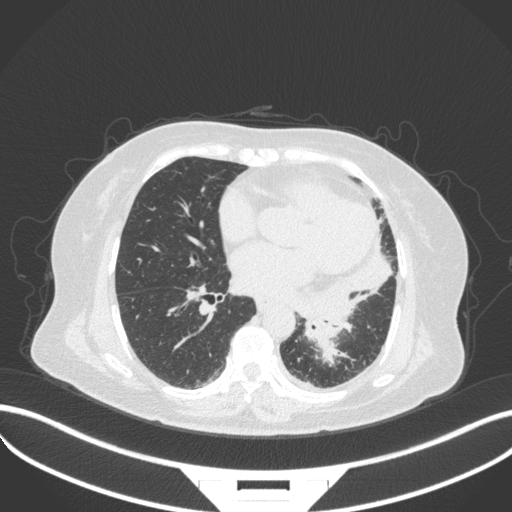
Chest CT, one axial slice; slice 154 of 328 in the series (ordered by position); 120 kVp; lung window (W 1500 / L -600 HU); 1 mm slice thickness; 512 × 512 image matrix. Patient: female, 69 years. From the clinical record (not read from this slice): clinical TNM (as recorded): T2b N3 M1.
Outlined on this slice (bounding box drawn by a radiologist):
- lung tumour (recorded histology: adenocarcinoma): bounding box [x1, y1, x2, y2] px = [297, 286, 348, 368]